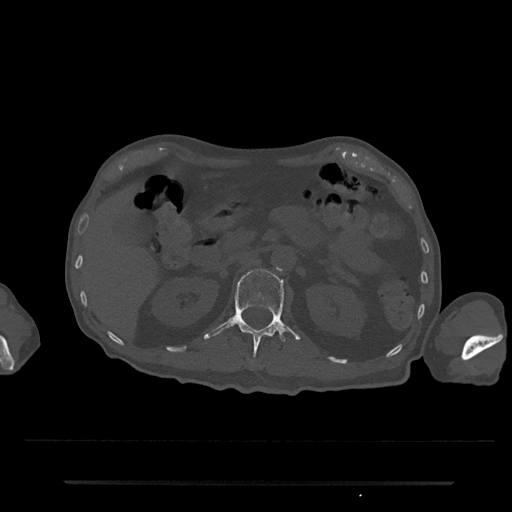
CT including the spine, one axial slice; position 129 of 797 along the scan axis; reconstruction kernel Br40s/3; 120 kVp; bone window (W 1800 / L 400 HU); 0.5 mm slice thickness; 512 × 512 image matrix, field of view 427 × 427 mm. Male patient, age 74 years. Case-level facts recorded for this patient, not image findings: primary cancer: prostate.
Structures marked on this image (semi-automatically segmented with operator editing):
- L1 vertebra: bounding box <204,269,301,355> (left, top, right, bottom; pixels)